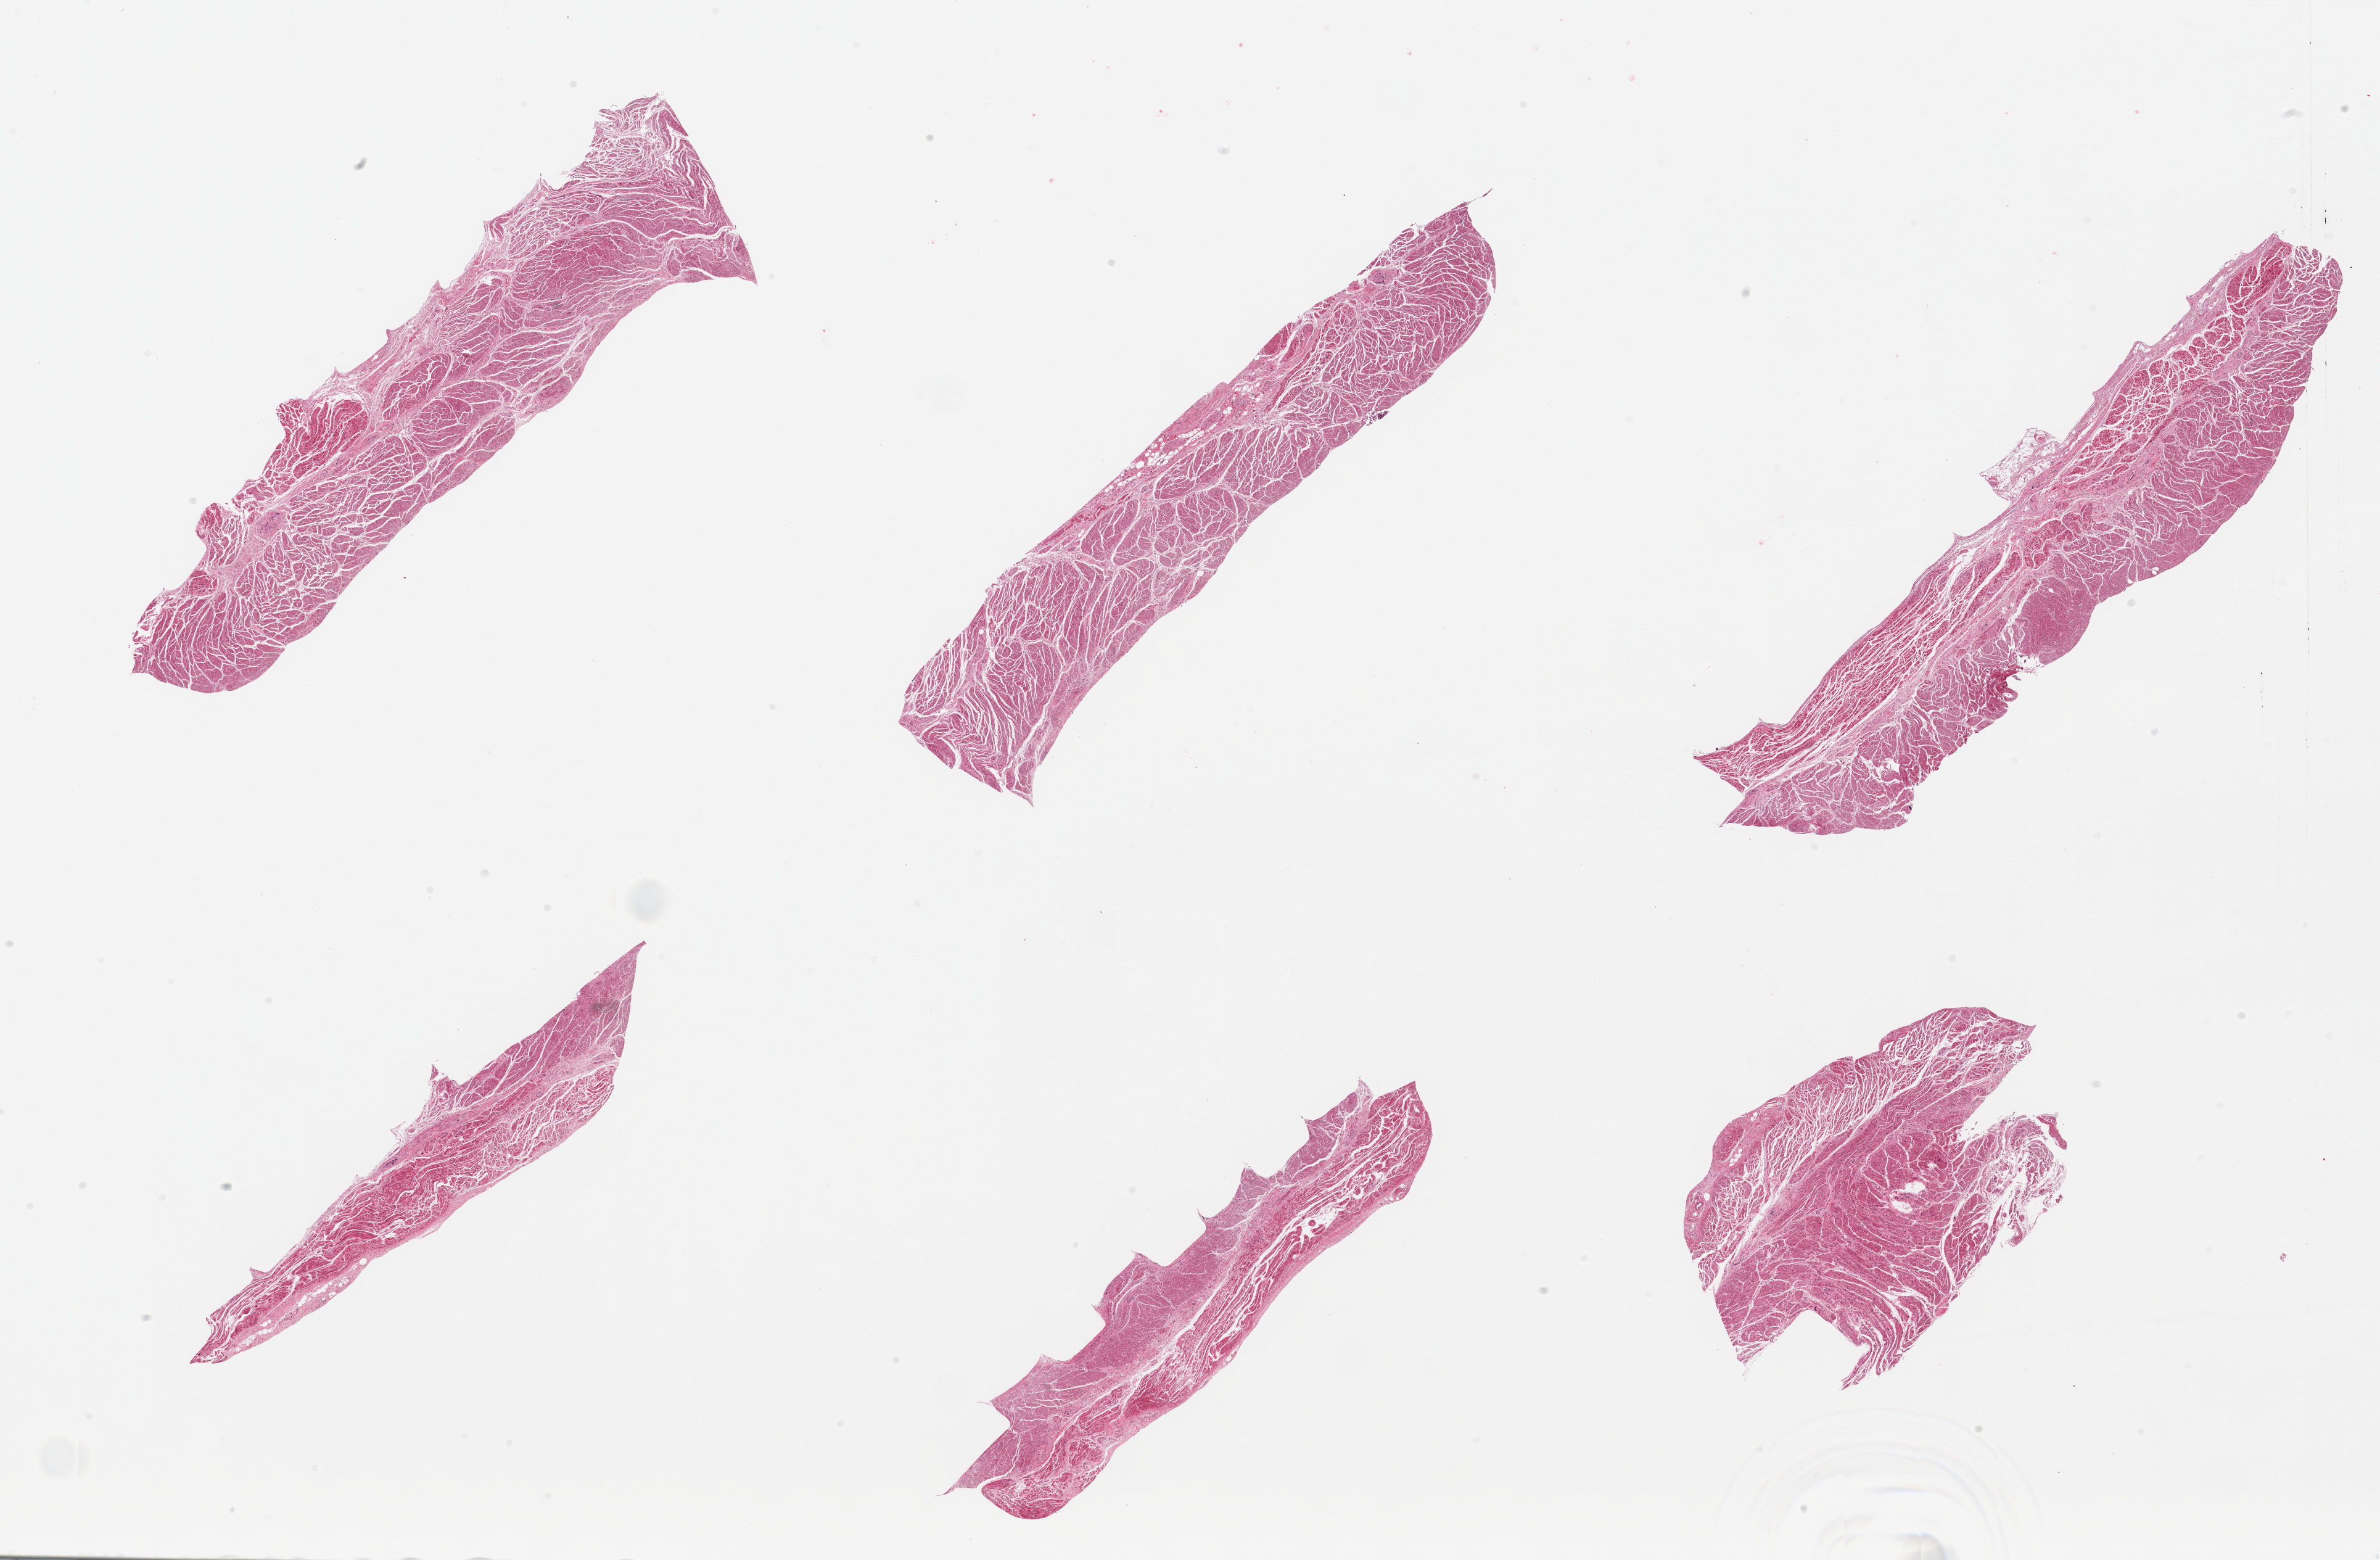
Digitized hematoxylin and eosin (H&E)-stained section — a low-resolution overview of the entire scanned area, about 30.5 x 20.0 mm; PAXgene-fixed, paraffin-embedded tissue; target tissue: gastroesophageal junction; donor tissue sample. Male donor.
- reviewer comment on this tissue sample: 6 pieces, all target muscularis